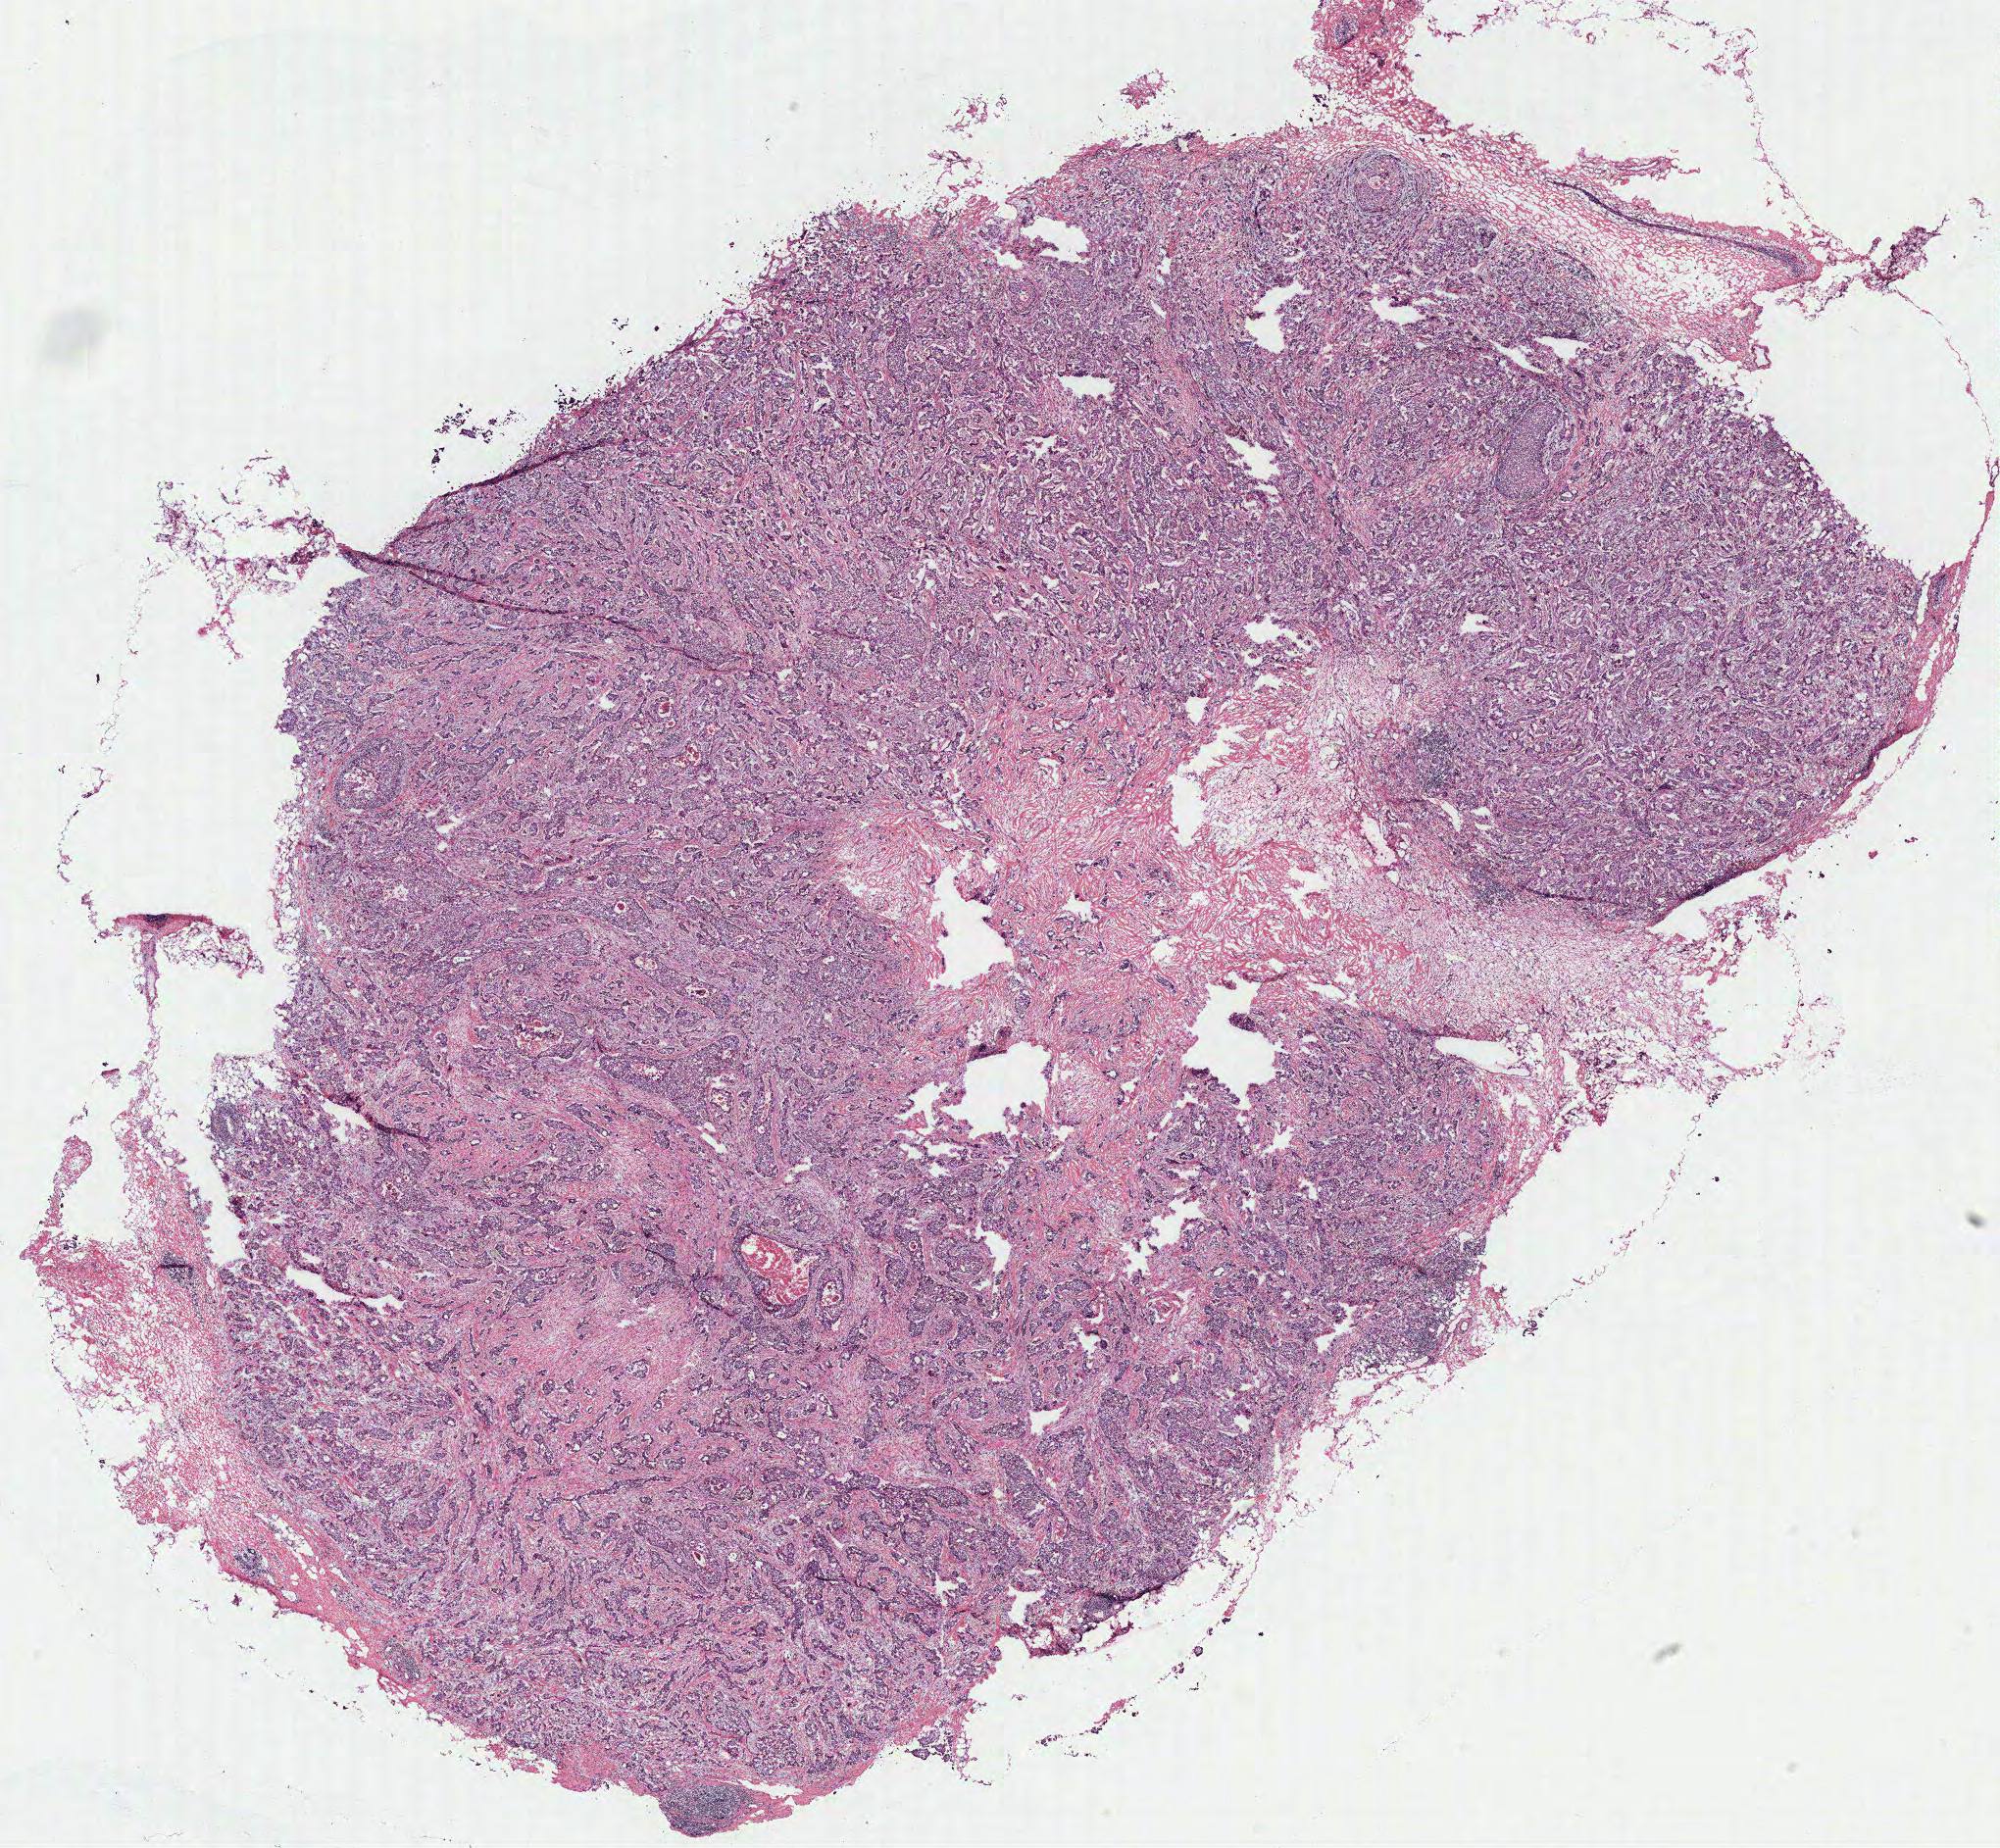
Whole-slide histology image, Hematoxylin and eosin (H&E) stained — a low-resolution overview of the entire scanned area, about 16.3 x 15.1 mm (from a 40x scan). Breast, tissue type not recorded. Patient: female, age 50 years.
Patient diagnosis: Infiltrating duct carcinoma, NOS.